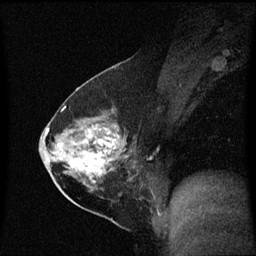
Breast MRI (dynamic contrast-enhanced), one sagittal slice; slice 32 of 60 in the series (ordered by position); dynamic contrast-enhanced series, image 2 of 3 at this slice position (ordered by acquisition); 1.5 T; TE 4.2 ms, TR 8.4 ms; 2 mm slice thickness; 256 × 256 image matrix, field of view 210 × 210 mm. Female patient, age 54 years. Case-level facts recorded for this patient, not image findings: setting: breast cancer imaged before/during neoadjuvant chemotherapy; receptor status: HER2-positive.
Structures marked on this image (semi-automatic segmentation, software-assisted and operator-edited):
- analysis volume of interest (the breast-tissue region the enhancement analysis was run in; not a lesion): bounding box [x1, y1, x2, y2] px = [59, 115, 138, 199]
- tumour enhancement mask (voxels above the 70 % enhancement threshold inside the analysis volume of interest): [59, 127, 121, 184]